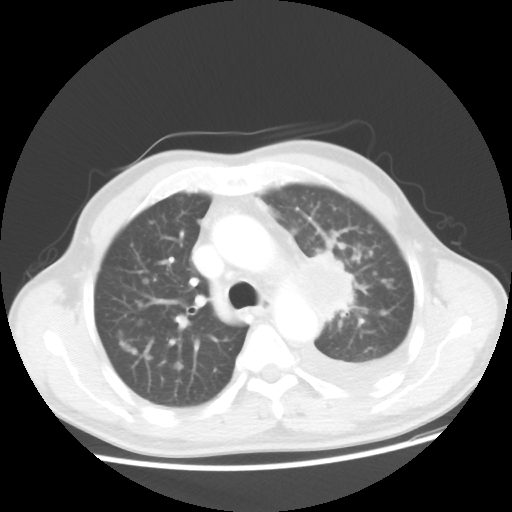
Chest CT, one axial slice. Slice 33 of 48 in the series (ordered by position). Reconstruction kernel STANDARD. 100 kVp. Lung window (W 1500 / L -600 HU). 5 mm slice thickness. 512 × 512 image matrix, field of view 362 × 362 mm. Patient: male, 55 years. From the clinical record (not read from this slice): clinical TNM (as recorded): T2 N3 M1a; histopathological grade: G3.
Outlined on this slice (rectangle marked by the reading radiologist):
- lung tumour (recorded histology: squamous cell carcinoma): box from (x=307, y=245) to (x=364, y=330) px